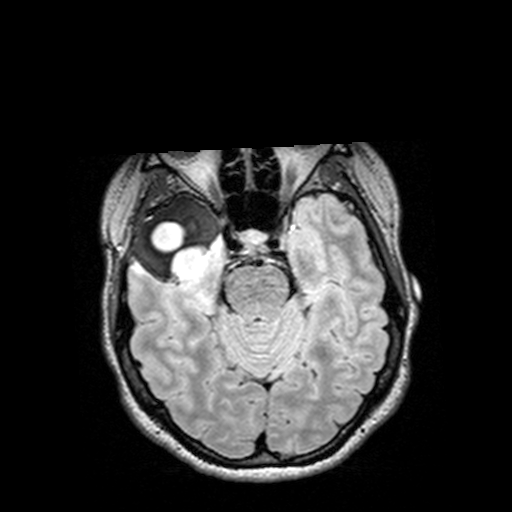
Brain MRI from a brain-tumour surgery series, one axial slice; slice 96 of 144 in the series (ordered by position); T2 FLAIR; 1 mm slice thickness; 512 × 512 image matrix, field of view 250 × 250 mm. From the clinical record (not read from this slice): histopathology: Astrocytoma; WHO grade: 3; IDH mutation: yes; tumour location: Right Insular Temporal.
Structures marked on this image (expert manual segmentation):
- tumour: bounding box <126,194,232,284> (left, top, right, bottom; pixels)